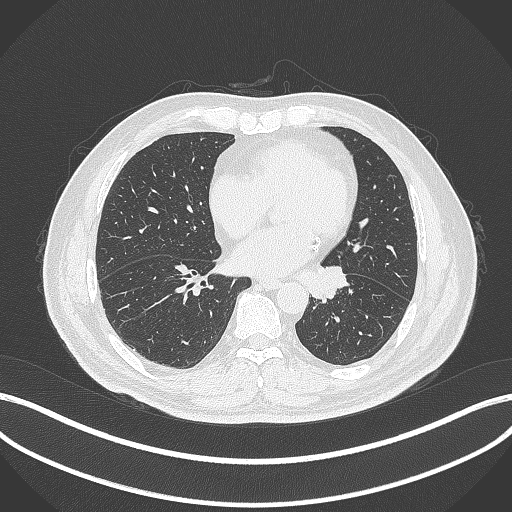
Chest CT, one axial slice. Slice 114 of 312 in the series (ordered by position). 120 kVp. Lung window (W 1500 / L -600 HU). 1 mm slice thickness. 512 × 512 image matrix, field of view 400 × 400 mm. Patient: male, 71 years. From the clinical record (not read from this slice): clinical TNM (as recorded): T1b N0 M0.
Outlined on this slice (bounding box drawn by a radiologist):
- lung tumour (recorded histology: squamous cell carcinoma): bounding box <306,265,350,303> (left, top, right, bottom; pixels)